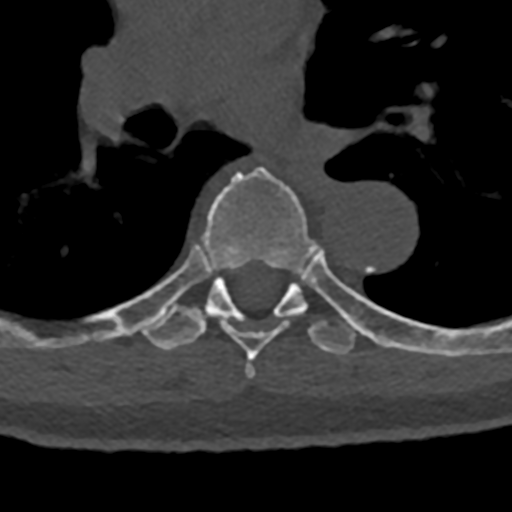
CT including the spine, one axial slice; 120 kVp; bone window (W 1800 / L 400 HU); 0.5 mm slice thickness; 512 × 512 image matrix. Male patient, age 74 years. Case-level facts recorded for this patient, not image findings: primary cancer: renal; vertebrae with lytic lesions (as recorded): T10, L1, L2, L3, L4, L5.
Annotated regions visible in this slice (semi-automatically segmented with operator editing):
- T6 vertebra: bounding box [x1, y1, x2, y2] px = [154, 166, 317, 379]
- T7 vertebra: [70, 246, 432, 355]